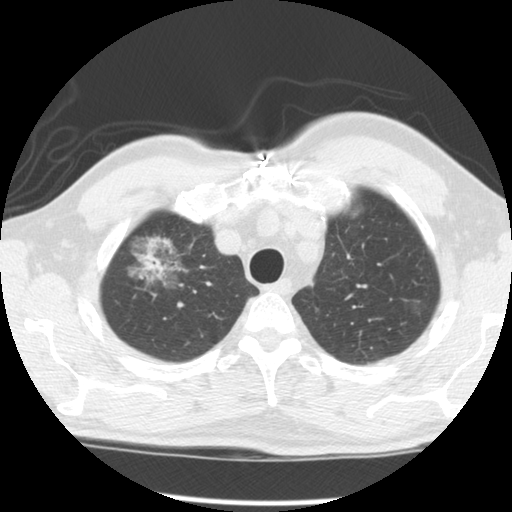
Axial slice from a low-dose chest CT screening exam. Second annual screen. Lung window (W 1500 / L -600 HU). 2.5 mm slice thickness. Standard (soft-tissue) reconstruction kernel (STANDARD). Slice 20 of 120 in the series. 512 × 512 image matrix. Male, age 64 years at enrolment.
Expert reader's lesion annotation, box from (x=121, y=228) to (x=196, y=300) px. The screening reader recorded 2 non-calcified nodules or masses ≥4 mm on this exam (right upper lobe, left upper lobe); which of them this box marks is not recorded. Official screen result: positive, other. Later outcome: lung cancer diagnosed 429 days after this screen — adenocarcinoma, NOS, right upper lobe, well differentiated (G1), stage IB (AJCC 6th edition), 45 mm at pathology.